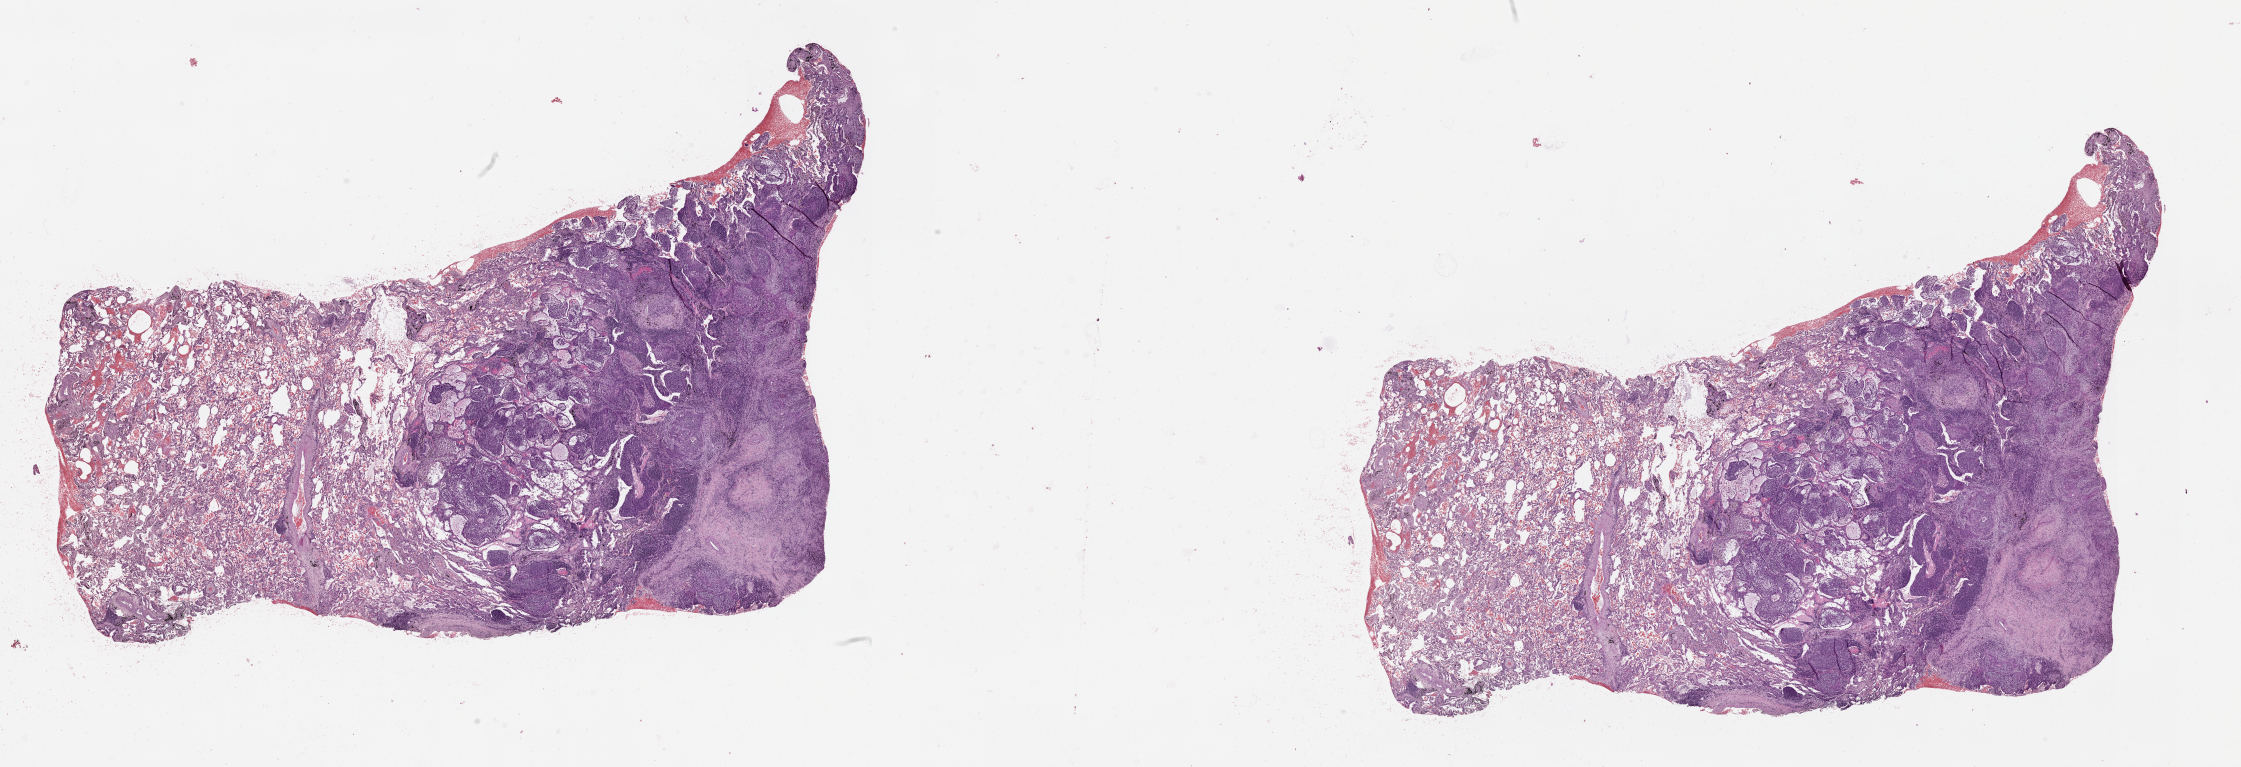
Digitized Hematoxylin and eosin (H&E) stained tissue section (whole slide) — whole scanned area (about 36.1 x 12.3 mm, acquisition: 20x scan) shown as a low-resolution overview; lung, tumour tissue. 63-year-old female patient.
Patient diagnosis (cohort enrolment): squamous cell carcinoma (lung).